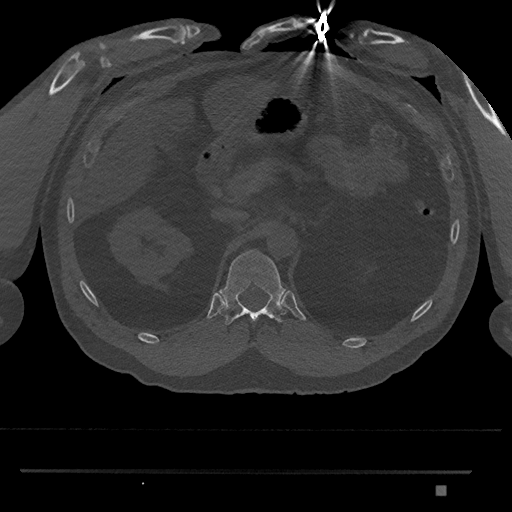
CT including the spine, one axial slice. Position 891 of 1134 along the scan axis. Bone window (W 1800 / L 400 HU). 0.5 mm slice thickness. 512 × 512 image matrix. Male patient, age 65 years. From the clinical record (not read from this slice): primary cancer: prostate.
Structures marked on this image (semi-automatic segmentation, software-assisted and operator-edited):
- T12 vertebra: bounding box [x1, y1, x2, y2] px = [219, 250, 288, 325]